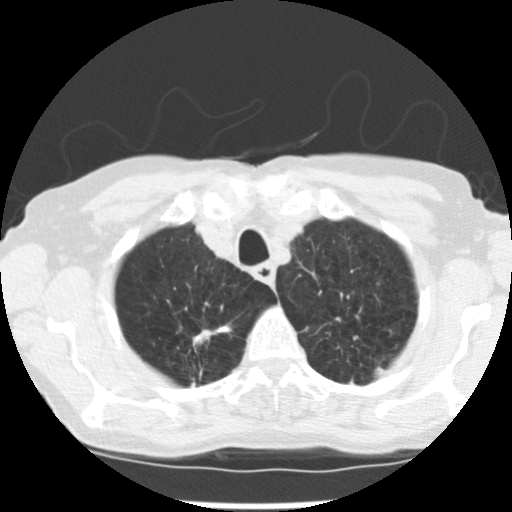
Chest CT (low-dose screening protocol), one axial image; first (baseline) screen; lung window (W 1500 / L -600 HU); 2.5 mm slice thickness; standard (soft-tissue) reconstruction kernel (STANDARD); 512 × 512 image matrix. Female participant, aged 72 years at enrolment. Current smoker at enrolment.
- Expert reader's lesion annotation, box from (x=179, y=313) to (x=232, y=353) px.
- The screening reader recorded 3 non-calcified nodules or masses ≥4 mm on this exam; which of them this box marks is not recorded.
- Official screen result: positive, change unspecified: nodule(s) >= 4 mm or enlarging nodule(s), mass(es), or other non-specific abnormalities suspicious for lung cancer.
- Lung cancer was diagnosed 50 days after this screen: adenocarcinoma, NOS, right upper lobe, moderately differentiated (G2), stage IB (AJCC 6th edition), 22 mm at pathology.